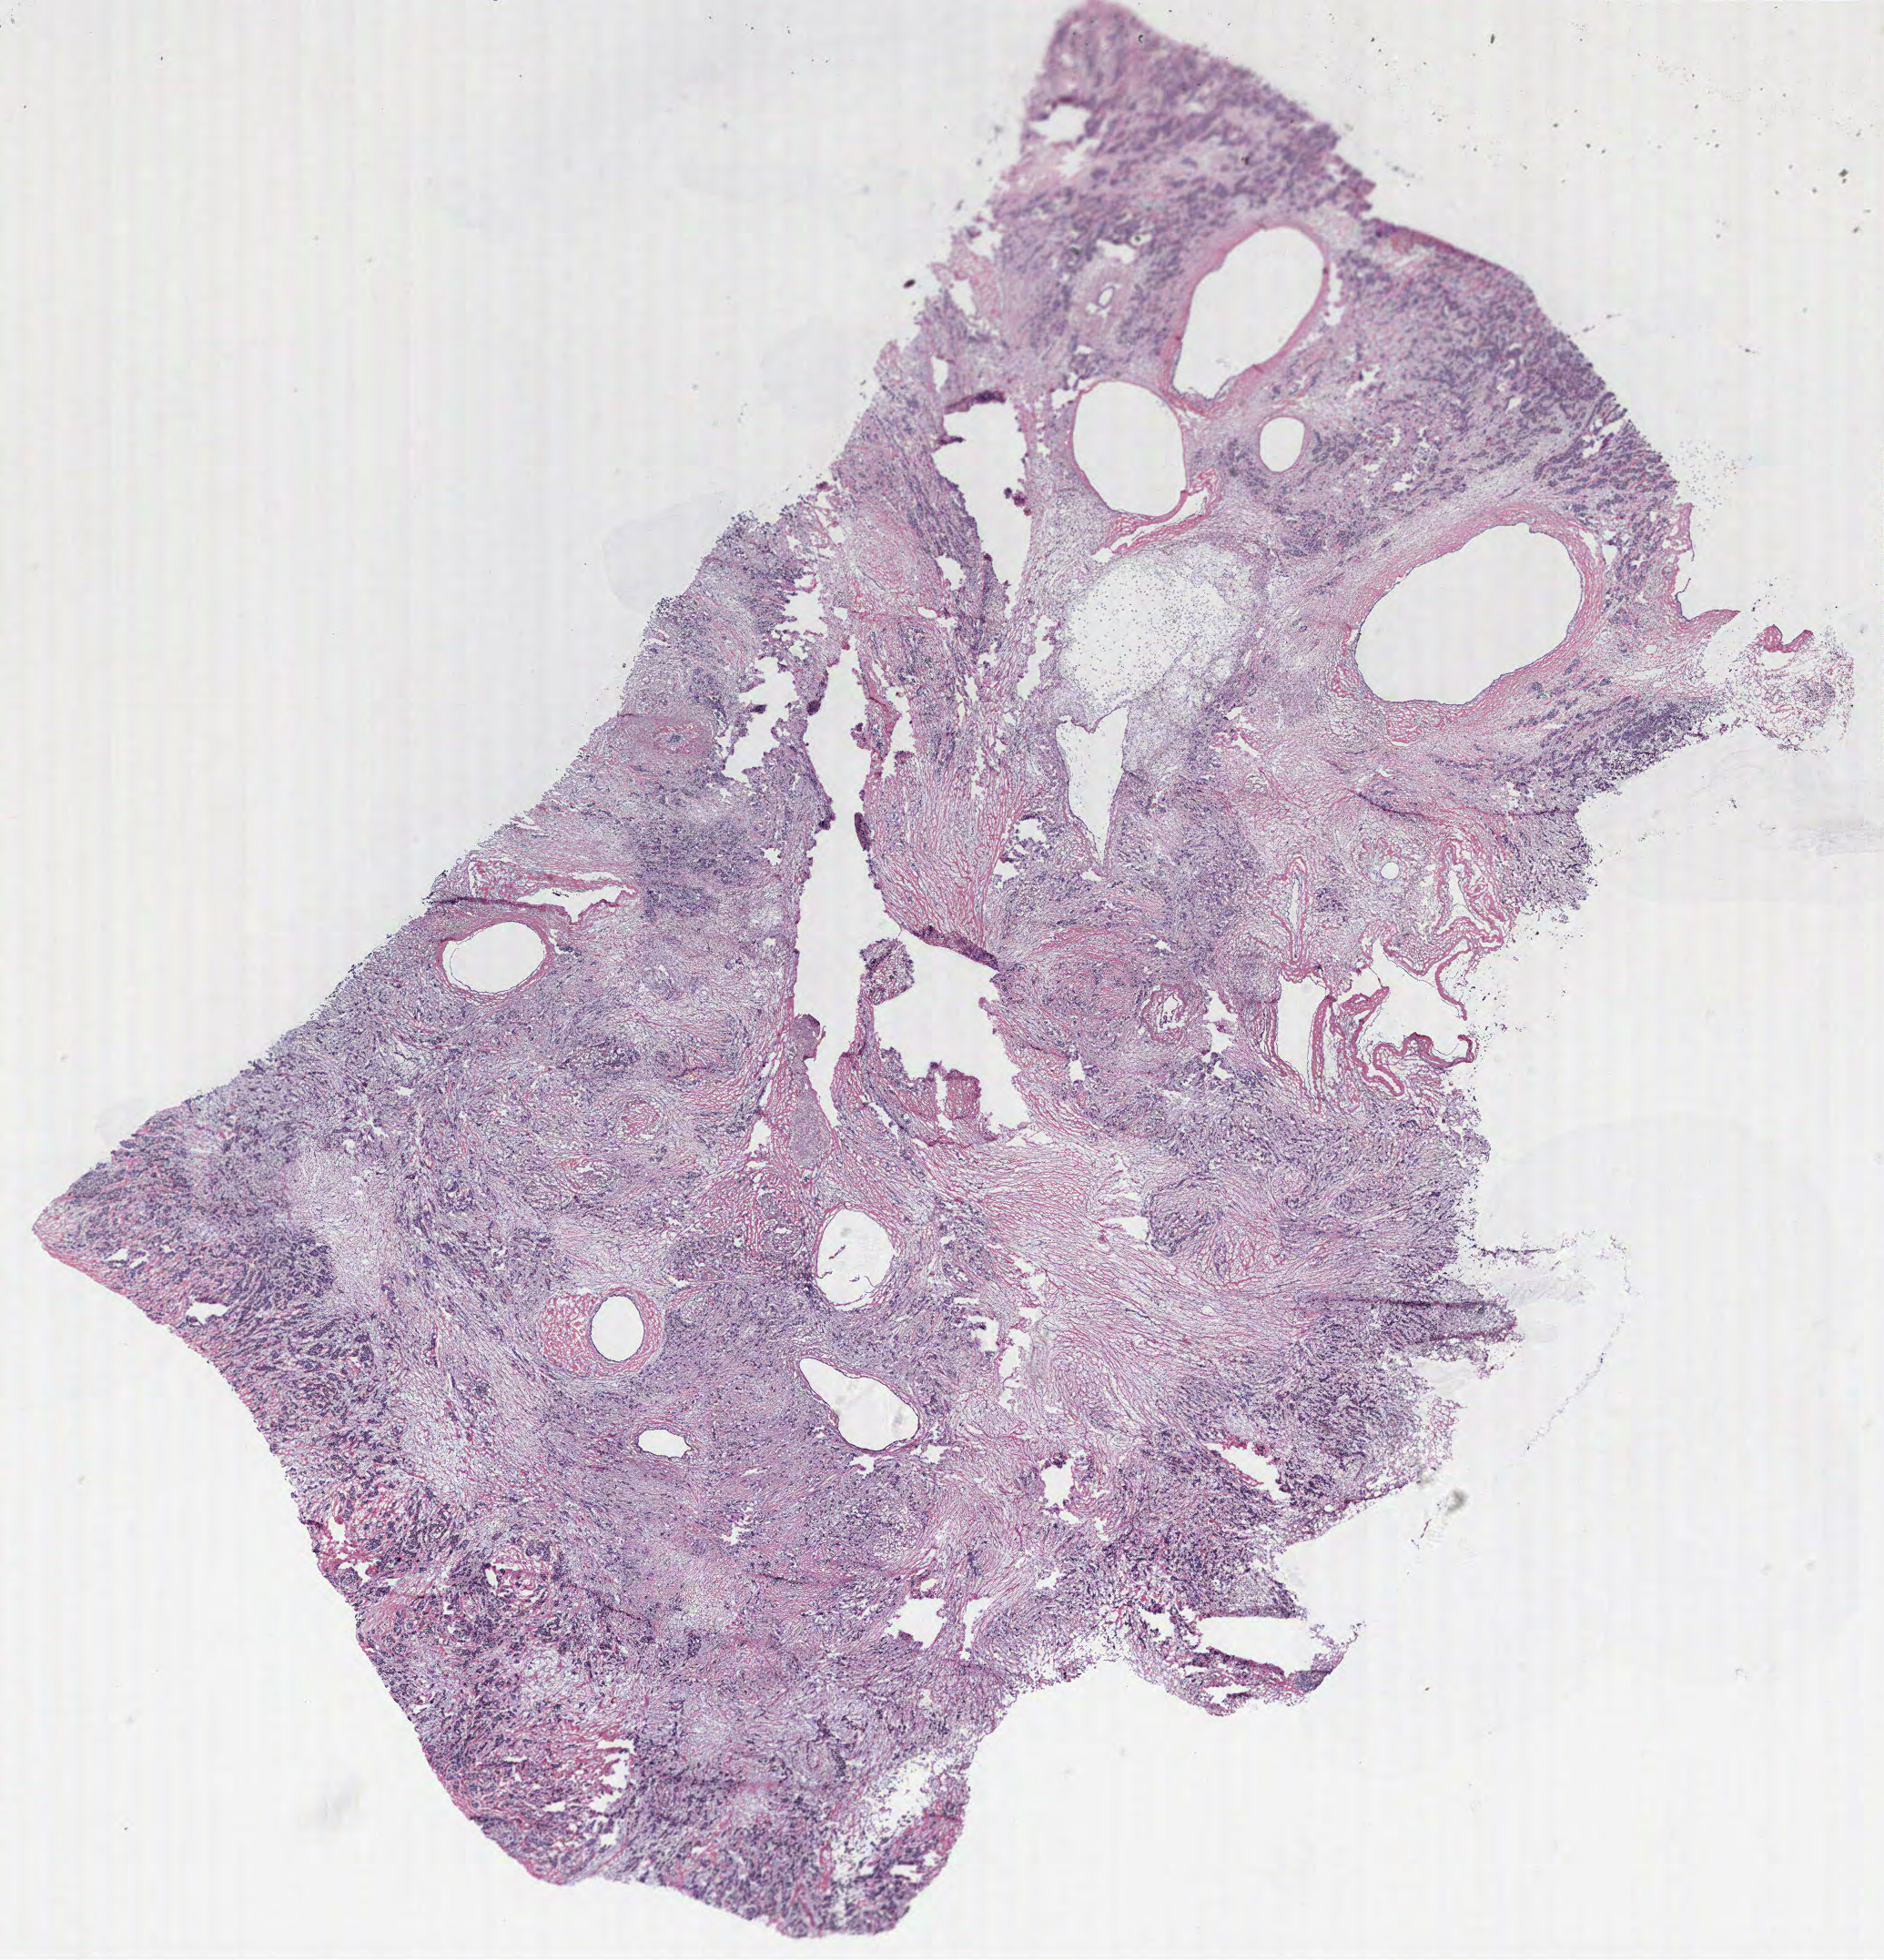
Whole-slide histology image, H&E-stained, a low-resolution overview of the entire scanned area, about 16.6 x 17.2 mm (from a 40x scan); breast, tissue type not recorded. Female, 40 y/o.
Patient diagnosis: Infiltrating duct carcinoma, NOS.